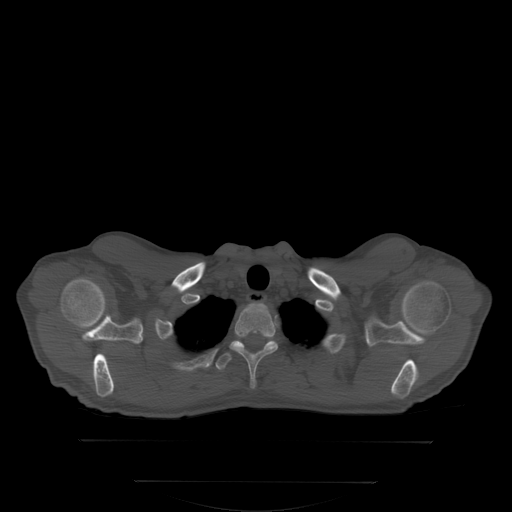
CT including the spine, one axial slice. Position 285 of 350 along the scan axis. Bone window (W 1800 / L 400 HU). 2.5 mm slice thickness. 512 × 512 image matrix. Male patient, age 58 years. From the clinical record (not read from this slice): primary cancer: prostate; vertebrae with lytic lesions (as recorded): L1.
Structures marked on this image (semi-automatically segmented with operator editing):
- T1 vertebra: bounding box <229,307,278,388> (left, top, right, bottom; pixels)
- T2 vertebra: <217,341,287,372>
- T3 vertebra: <215,355,225,364>